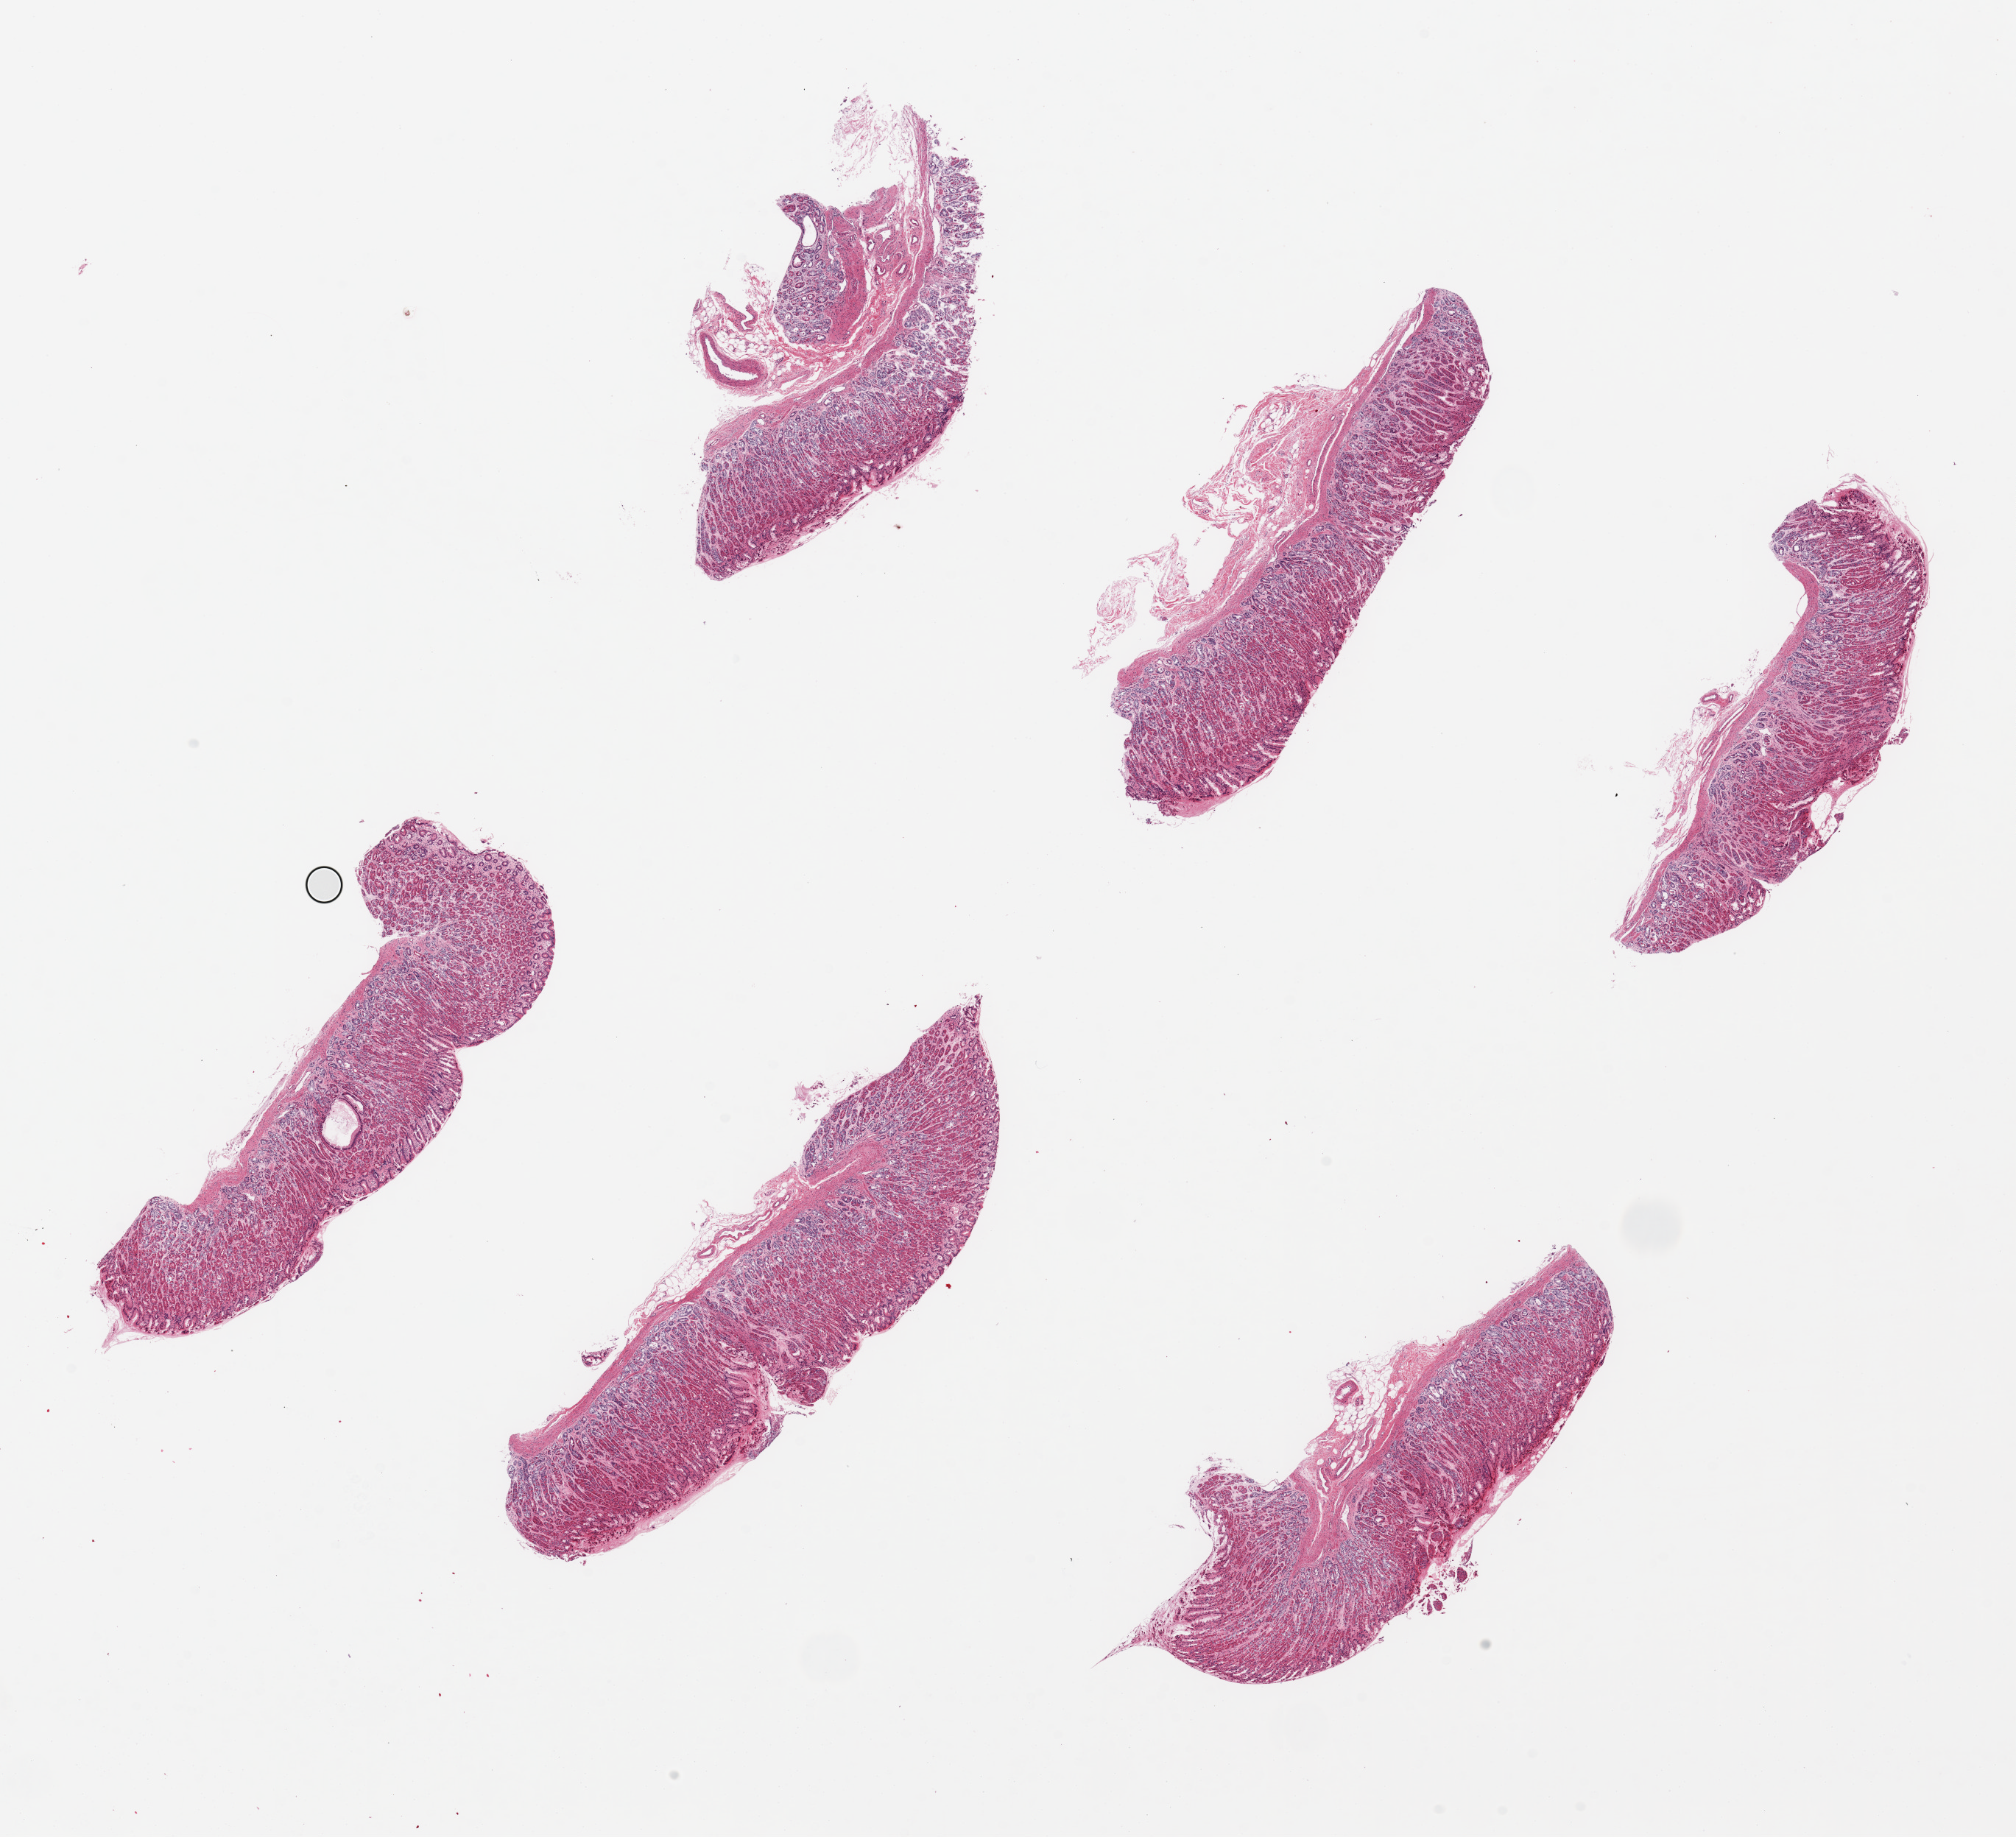
Whole-slide image, hematoxylin and eosin (H&E) stain — shown as a low-resolution overview of the whole scanned area (about 21.7 x 19.7 mm, acquisition: 20x scan), PAXgene-fixed paraffin-embedded (PFPE) section, sampled site (target tissue): stomach, tissue donor sample. Male donor.
Pathologist's review note for this sample: 6 pieces ~7x1.5mm nearly all mucosa and fairly well preserved-- mucosa is 75-100% of thickness.